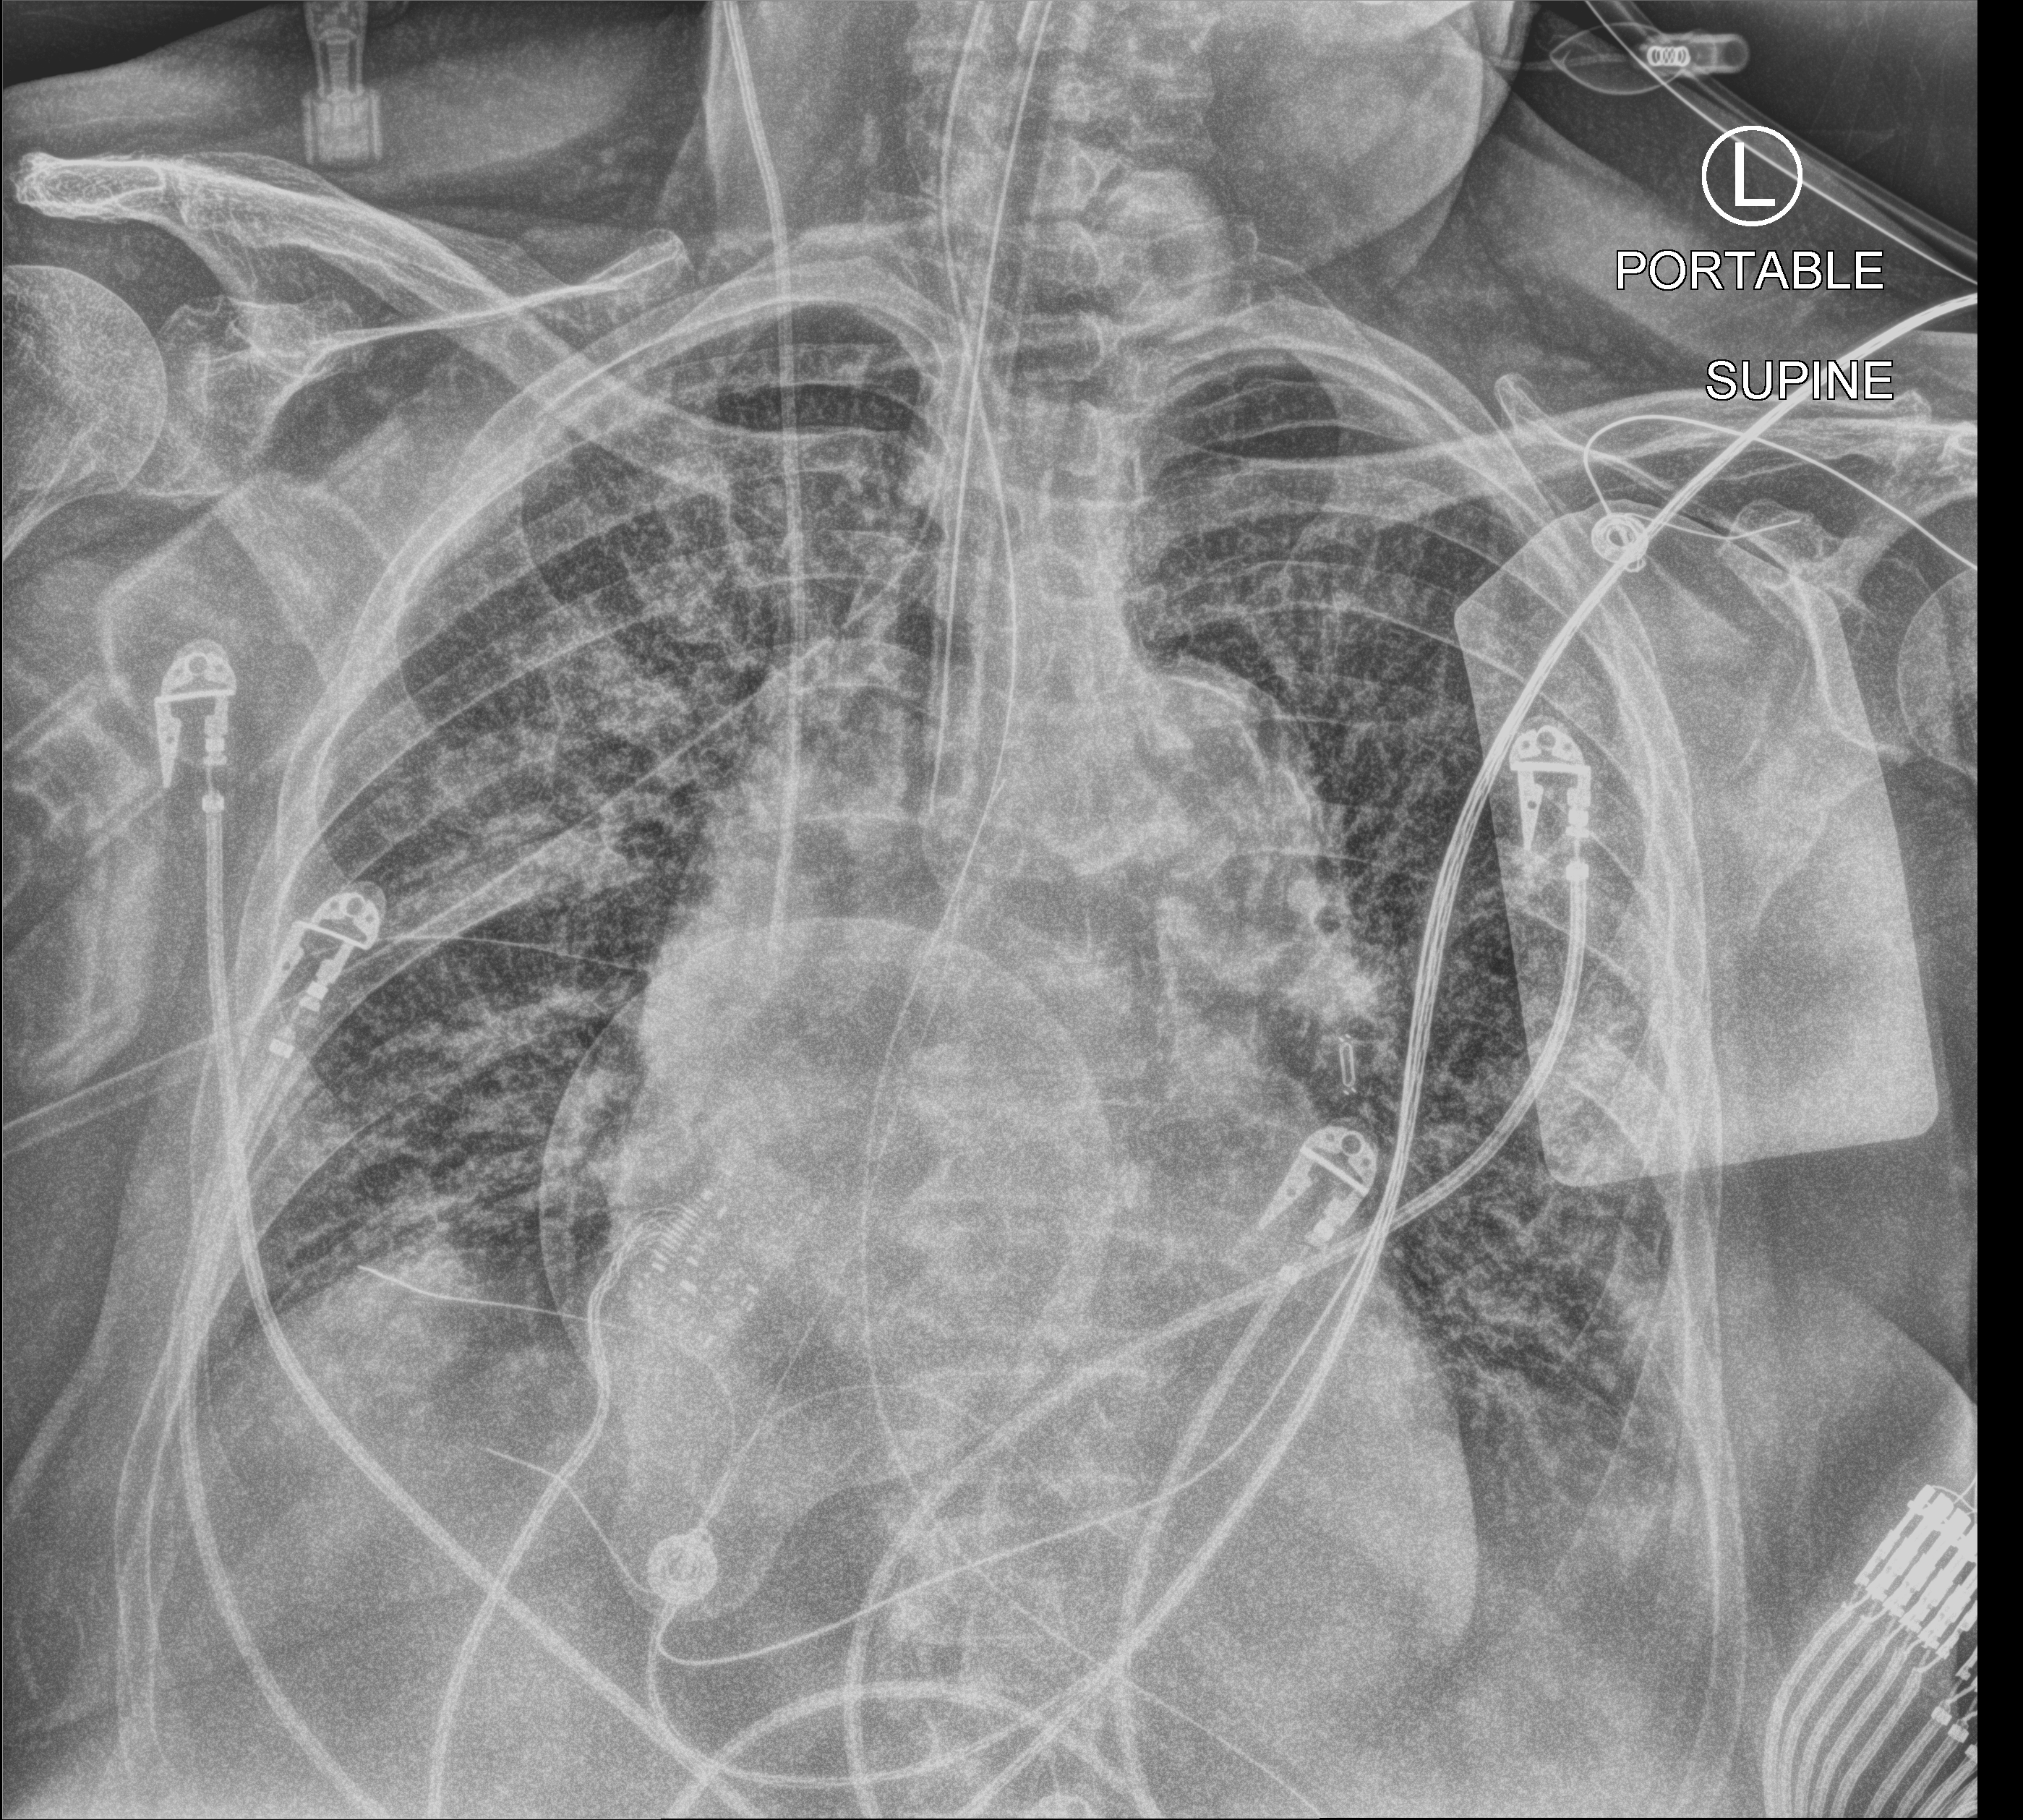
Chest X-ray (portable). Female patient hospitalised with COVID-19, age 75–90 years.
Hospital-stay facts (about this admission, not read from this image; timing relative to this image not recorded): mechanically ventilated during this hospital stay: yes.